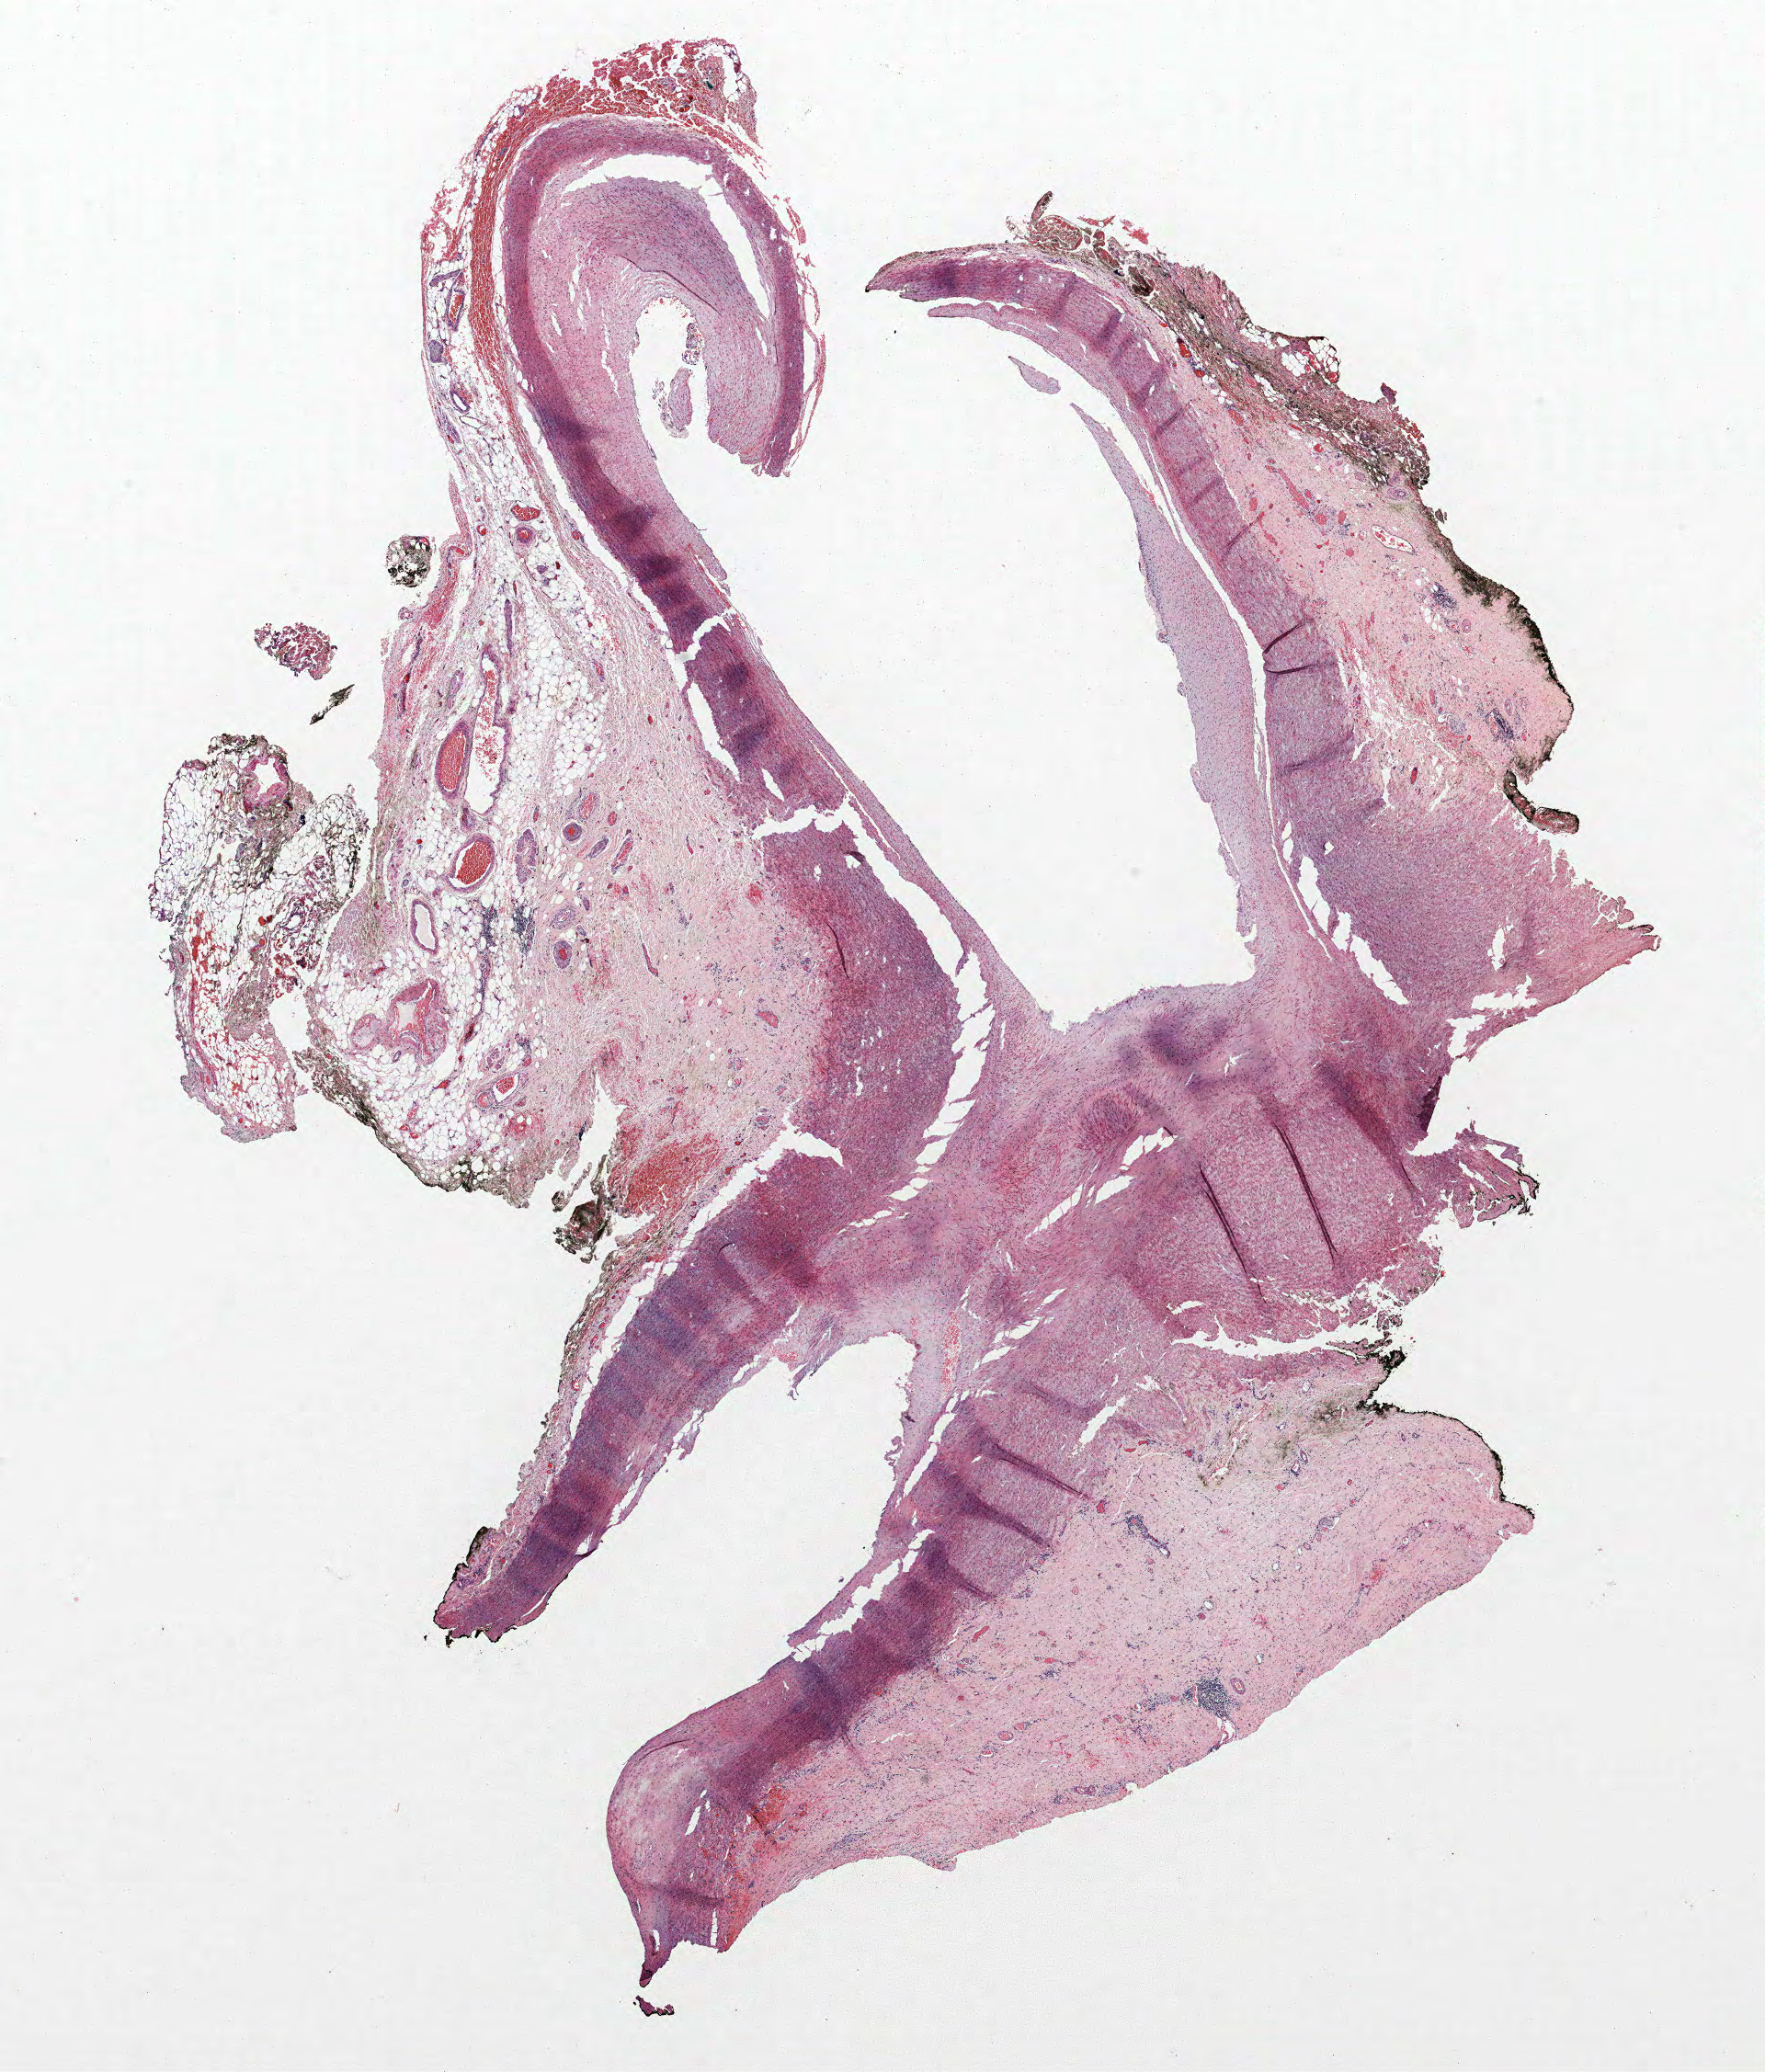
Whole-slide histology image, H&E — a low-resolution overview of the entire scanned area, about 15.4 x 18.0 mm. Formalin-fixed paraffin-embedded (FFPE) section. Lung tissue. Male patient, aged 68 at enrolment. Former smoker at enrolment. Grade: poorly differentiated (G3).
Participant's lung-cancer diagnosis: Squamous cell carcinoma, NOS (ICD-O-3 8070/3). Stage (AJCC 6th edition): IIB. Tumour size (pathology): 35 mm. ICD-O-3 topography: upper lobe of lung (C34.1). Primary tumour location (clinical record): left upper lobe.